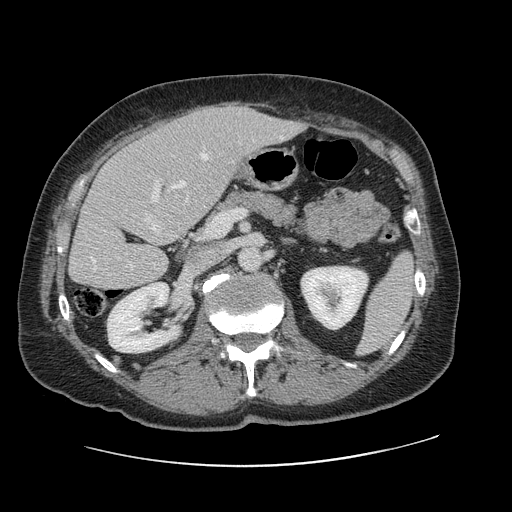
Contrast-enhanced abdominal CT, one axial slice. Position 50 of 138 along the scan axis. 120 kVp. Intravenous contrast given. Soft-tissue window (W 400 / L 40 HU). 2.5 mm slice thickness. 512 × 512 image matrix. Male patient, age 71 years. From the clinical record (not read from this slice): diagnosis: colorectal cancer liver metastases, imaged before liver resection; multiple liver metastases: no; largest metastasis: 3.3 cm; disease in both lobes: no.
Annotated regions visible in this slice (manually delineated by an expert):
- hepatic veins: bounding box <91,154,227,270> (left, top, right, bottom; pixels)
- liver: <70,104,300,291>
- planned liver remnant (the part of the liver to remain after resection): <70,141,198,291>
- portal vein (with intrahepatic branches): <151,180,160,203>